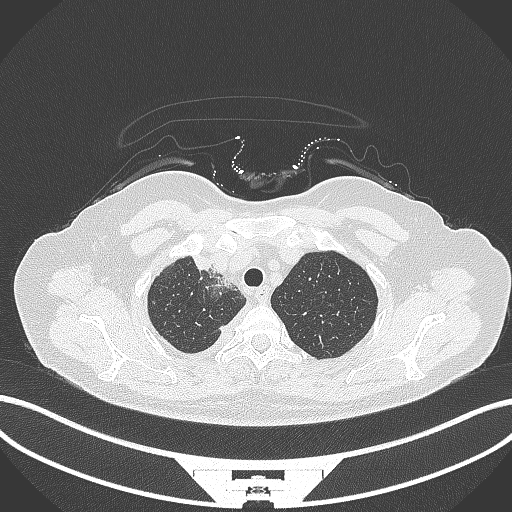
Chest CT, one axial slice. Slice 265 of 305 in the series (ordered by position). Reconstruction kernel B70f. 120 kVp. Lung window (W 1500 / L -600 HU). 512 × 512 image matrix. Patient: female, 52 years. From the clinical record (not read from this slice): clinical TNM (as recorded): T3 N1 M1.
Outlined on this slice (rectangle marked by the reading radiologist):
- lung tumour (recorded histology: adenocarcinoma): box from (x=183, y=250) to (x=215, y=274) px